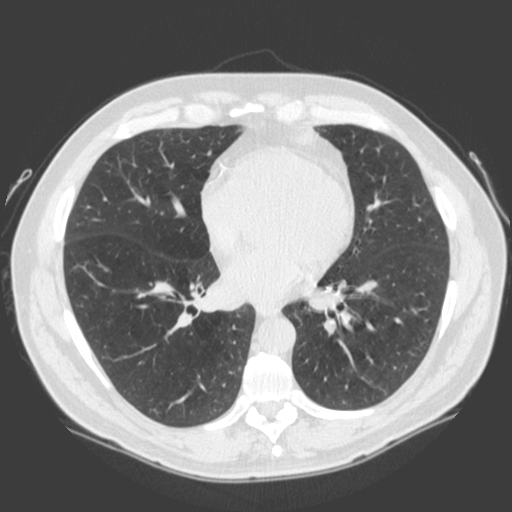
Low-dose screening chest CT, one axial slice. Slice 82 of 185 in the series (ordered by position). Lung window (W 1500 / L -600 HU). 2 mm slice thickness. 512 × 512 image matrix, field of view 360 × 360 mm.
Outlined on this slice (outlined manually by an expert reader):
- lesion 1 (tumor, lower lobe of left lung): bounding box <289,127,323,148> (left, top, right, bottom; pixels)